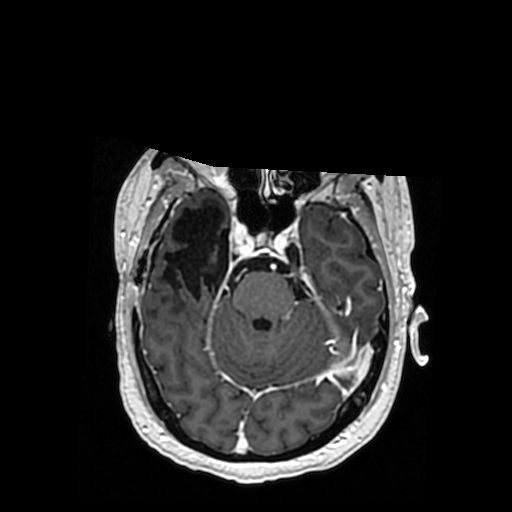
Brain MRI from a brain-tumour surgery series, one axial slice; position 237 of 364 along the scan axis; T1-weighted post-contrast; 0.5 mm slice thickness; 512 × 512 image matrix. Case-level facts recorded for this patient, not image findings: histopathology: Oligodendroglioma; WHO grade: 3; IDH mutation: yes; tumour location: Right Posterior Temporal Inferior Parietal.
Annotated regions visible in this slice (outlined manually by an expert reader):
- previous resection cavity: bounding box <161,206,229,304> (left, top, right, bottom; pixels)